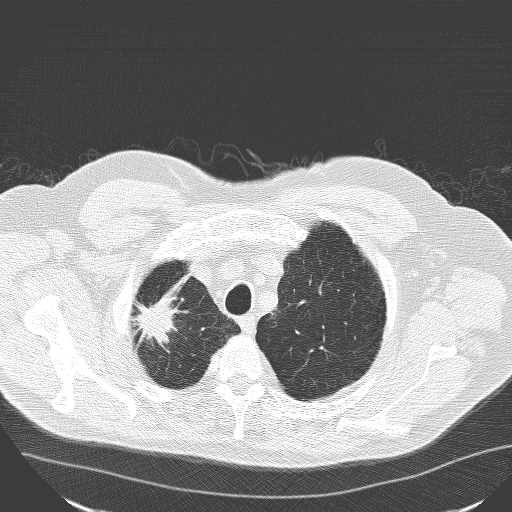
Chest CT (low-dose screening protocol), one axial image; baseline screening round; lung window (W 1500 / L -600 HU); 3.2 mm slice thickness; lung (sharp) reconstruction kernel (D); slice 140 of 160 in the series. Male participant, aged 71 years at enrolment. Current smoker at enrolment.
Expert-annotated lung lesion, bounding box <118,286,189,360> (left, top, right, bottom; pixels). Screening reader's record for this exam (one nodule recorded; not confirmed to be the boxed lesion): non-calcified nodule or mass ≥4 mm, right upper lobe, 30 × 25 mm, spiculated (stellate) margins, soft tissue attenuation. Participant outcome: lung cancer diagnosed 182 days after this screen — squamous cell carcinoma, NOS, right upper lobe, poorly differentiated (G3), stage IA (AJCC 6th edition), 30 mm at pathology.